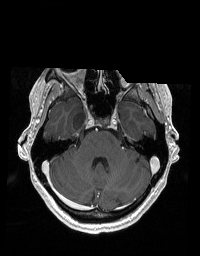
Brain MRI from a brain-tumour surgery series, one axial slice. Position 132 of 192 along the scan axis. T1-weighted post-contrast. 1 mm slice thickness. 200 × 256 image matrix. From the clinical record (not read from this slice): histopathology: Glioblastoma; WHO grade: 2.
Structures marked on this image (expert manual segmentation):
- tumour: bounding box [x1, y1, x2, y2] px = [73, 108, 86, 131]